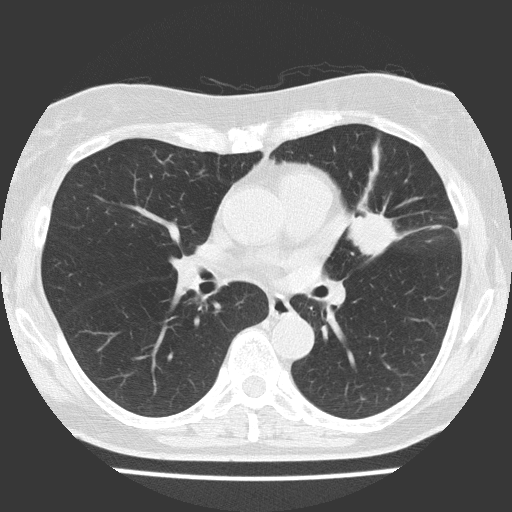
Axial slice from a low-dose chest CT screening exam, first (baseline) screen, lung window (W 1500 / L -600 HU), lung (sharp) reconstruction kernel (FC51), slice 72 of 151 in the series, 512 × 512 image matrix. Female, age 70 years at enrolment. Current smoker at enrolment.
• Expert-annotated lung lesion, bounding box [x1, y1, x2, y2] px = [322, 180, 432, 274].
• The screening reader recorded 2 non-calcified nodules or masses ≥4 mm on this exam (left upper lobe, right upper lobe); which of them this box marks is not recorded.
• Official screen result: positive, change unspecified: nodule(s) >= 4 mm or enlarging nodule(s), mass(es), or other non-specific abnormalities suspicious for lung cancer.
• Participant outcome: lung cancer diagnosed 25 days after this screen — adenocarcinoma, NOS, left upper lobe, poorly differentiated (G3), stage IV (AJCC 6th edition), 30 mm at pathology.